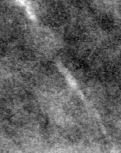
Crop from a digitized film mammogram around one marked abnormality; left breast; CC view; BI-RADS breast density category 2 (scale 1–4).
Calcifications, morphology fine linear branching, distribution clustered / linear; BI-RADS assessment category 4; pathology result (as recorded, not read from the image): malignant.